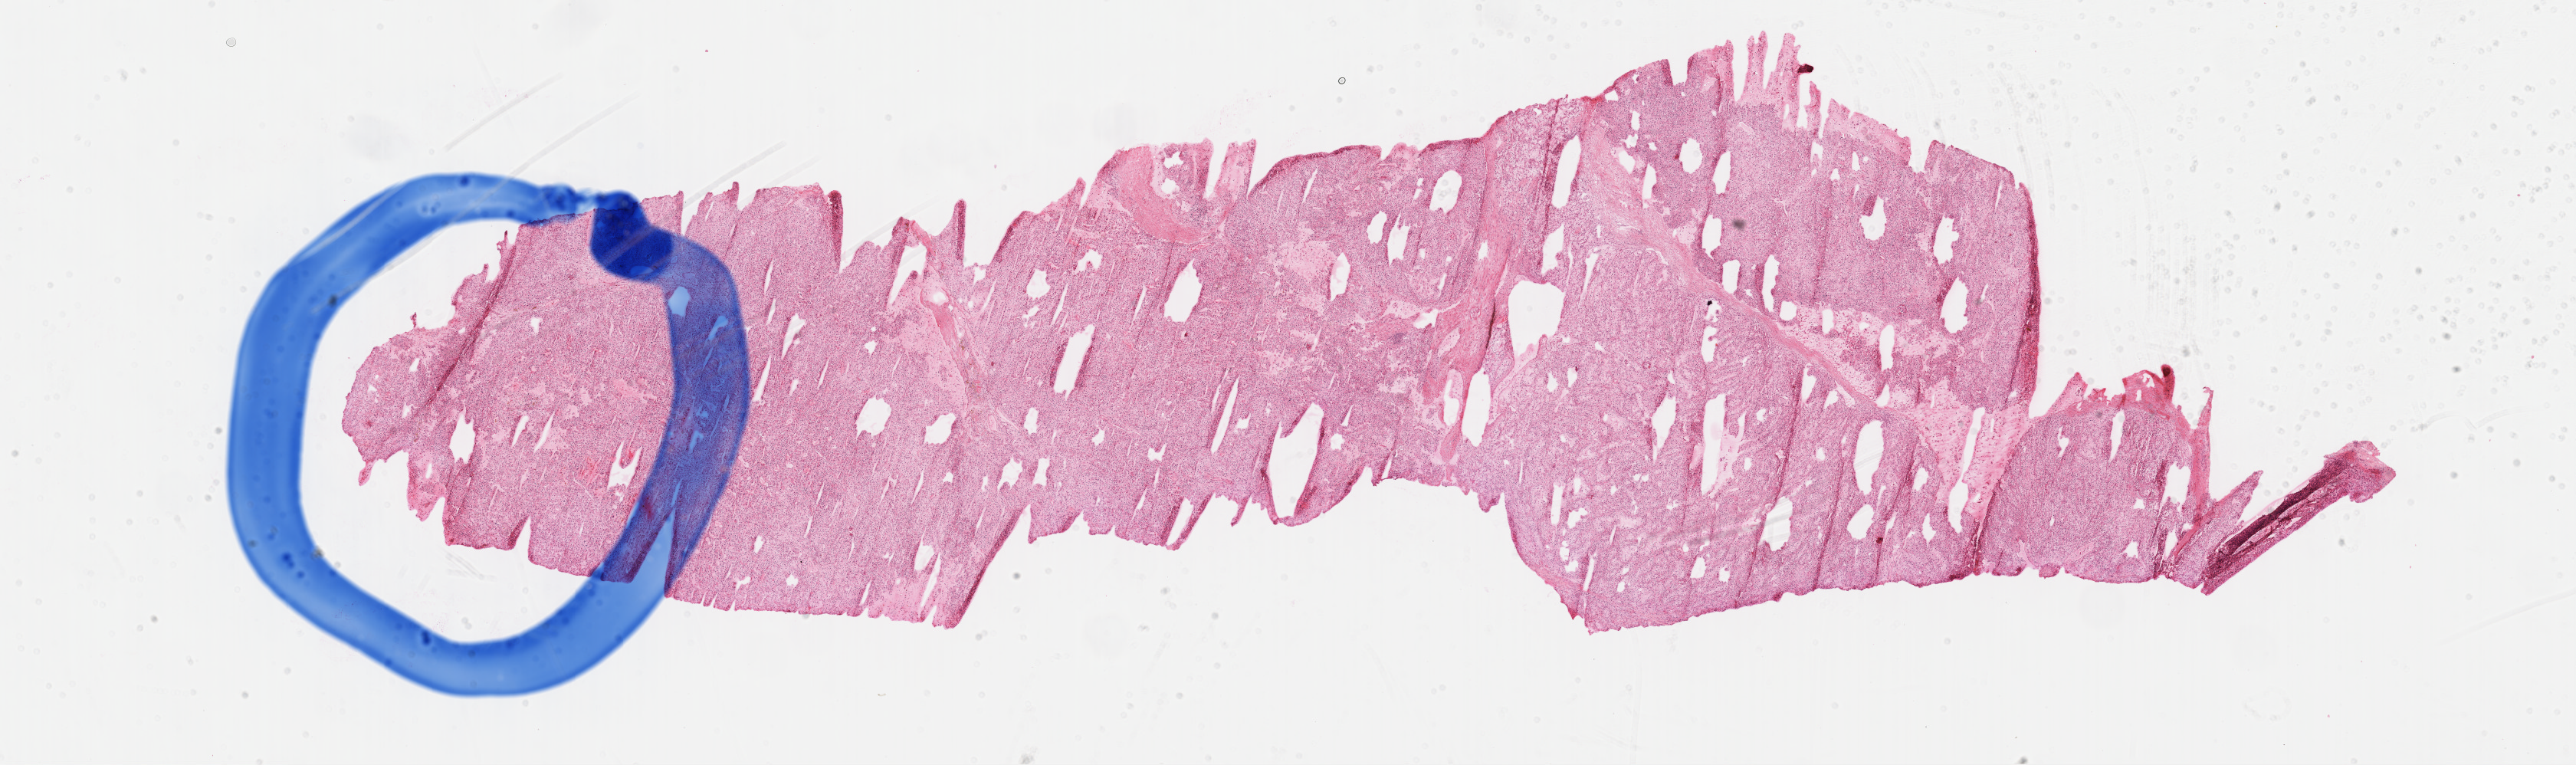
Whole-slide histology image, Hematoxylin and eosin (H&E) stained — shown as a low-resolution overview of the whole scanned area (about 27.2 x 8.1 mm), formalin-fixed paraffin-embedded (FFPE) diagnostic section, kidney, primary tumour sample. Male patient; age at initial diagnosis 60 years. Histologic grade: G4 (undifferentiated).
AJCC pathologic stage: IV (7th edition). Laterality: left. Pathologic diagnosis: Clear cell adenocarcinoma, NOS.